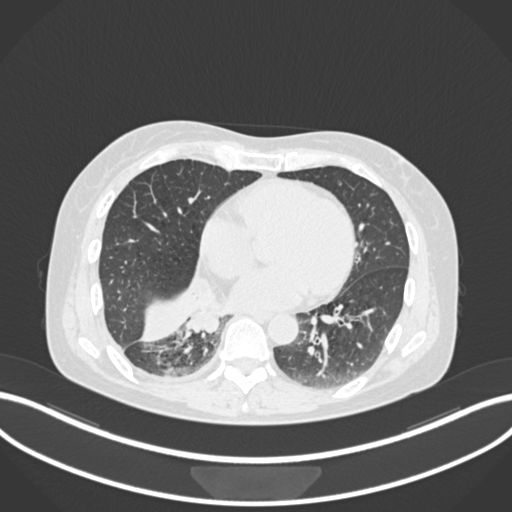
Chest CT, one axial slice; slice 60 of 168 in the series (ordered by position); reconstruction kernel B30f; lung window (W 1500 / L -600 HU); 512 × 512 image matrix, field of view 400 × 400 mm. Patient: female, 63 years. Case-level facts recorded for this patient, not image findings: clinical TNM (as recorded): T1c N0 M0.
Annotated regions visible in this slice (rectangle marked by the reading radiologist):
- lung tumour (recorded histology: adenocarcinoma): box from (x=179, y=302) to (x=226, y=342) px